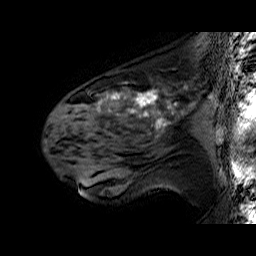
Breast MRI (dynamic contrast-enhanced), one sagittal slice; slice 38 of 60 in the series (ordered by position); dynamic contrast-enhanced series, time point 2 of 6 at this slice position (early post-contrast); 1.5 T; TE 6.4 ms, TR 32.9 ms; 256 × 256 image matrix. Female patient. Case-level facts recorded for this patient, not image findings: setting: breast cancer imaged before/during neoadjuvant chemotherapy; receptor status: HER2-positive.
Annotated regions visible in this slice (semi-automatic segmentation, software-assisted and operator-edited):
- analysis volume of interest (the breast-tissue region the enhancement analysis was run in; not a lesion): bounding box <51,78,196,160> (left, top, right, bottom; pixels)
- tumour enhancement mask (voxels above the 100 % enhancement threshold inside the analysis volume of interest): <97,90,171,125>